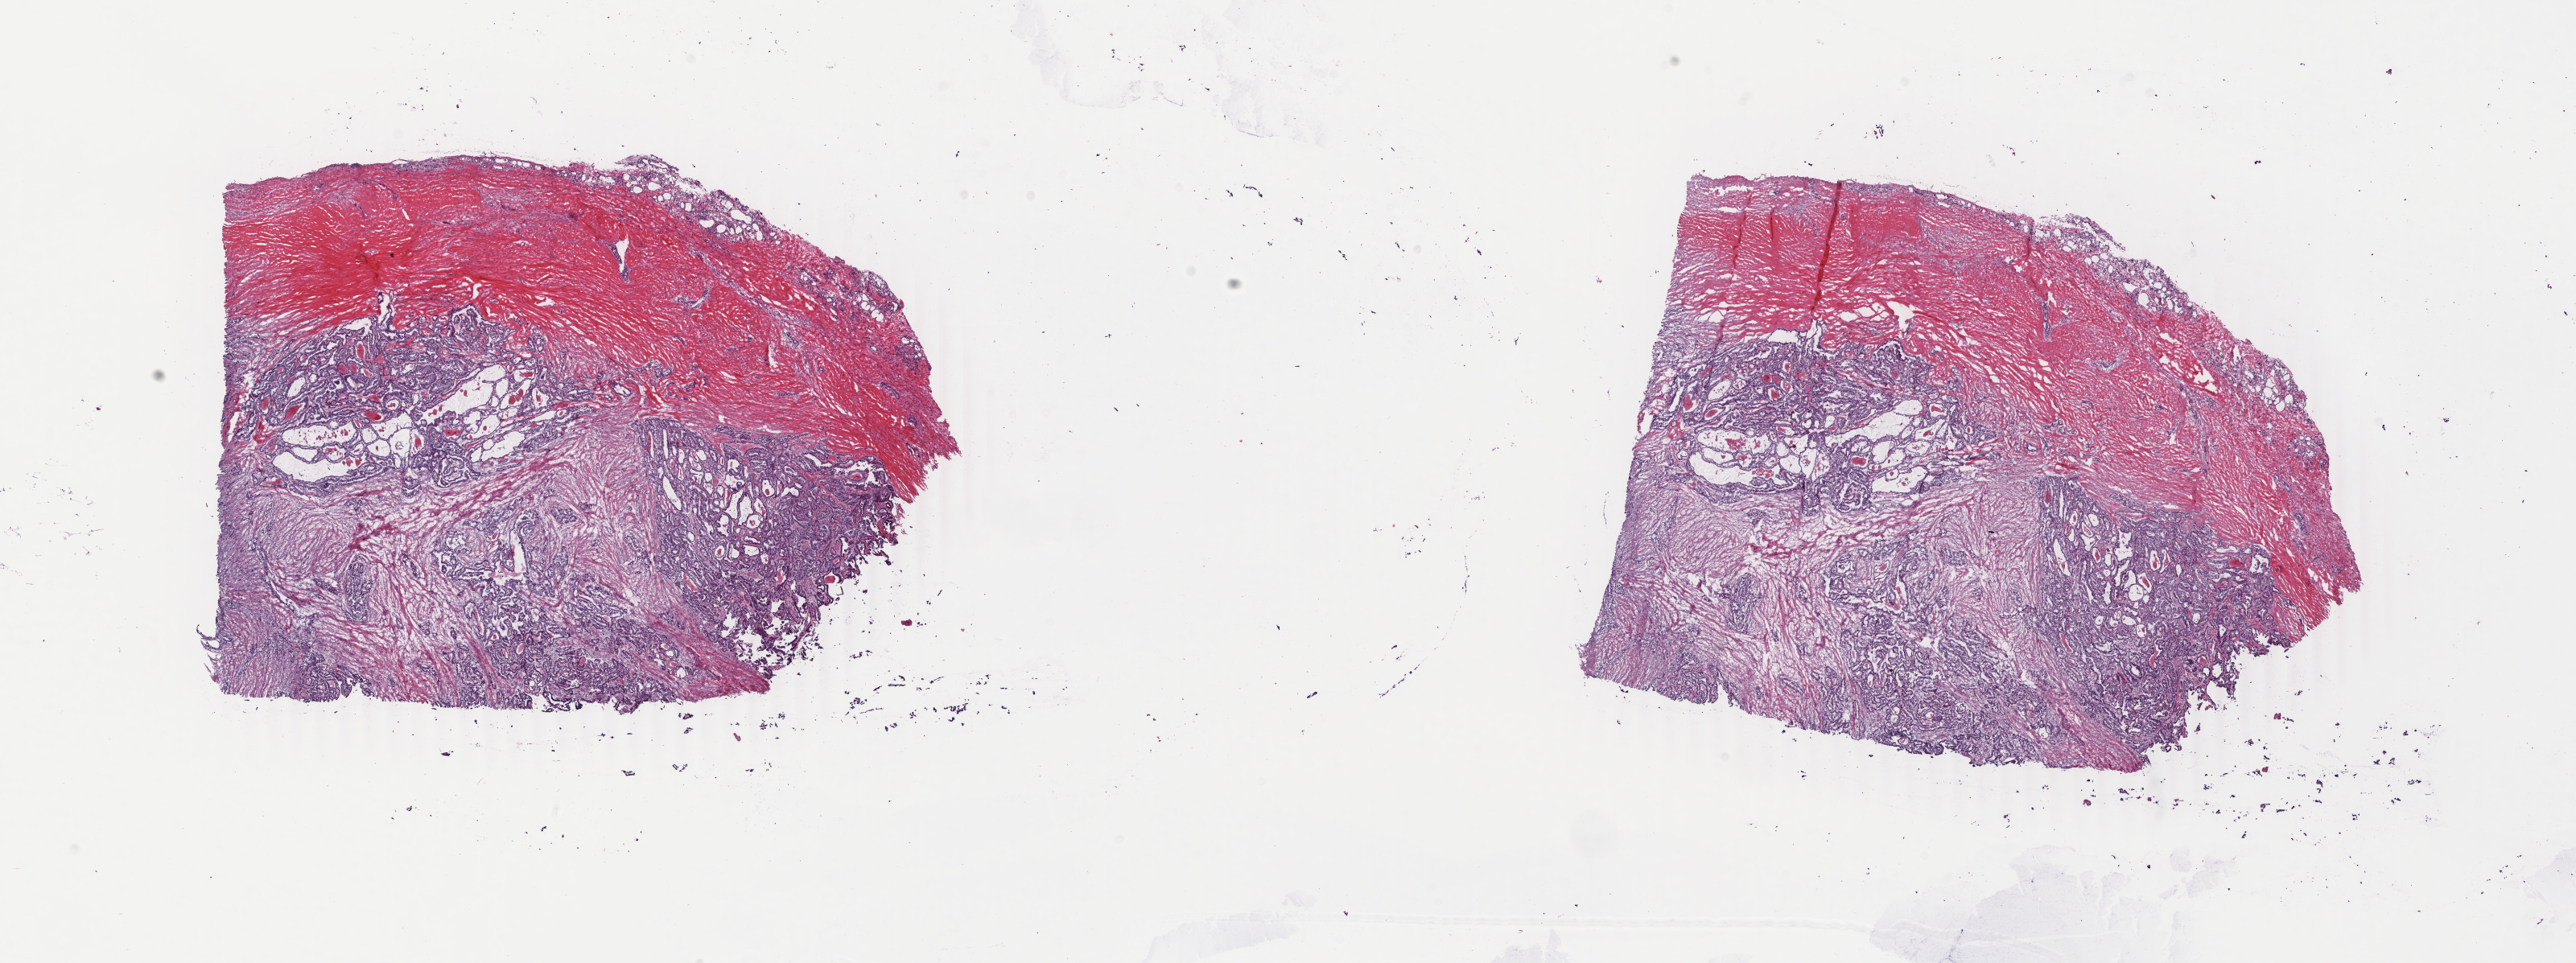
Whole-slide histology image, H&E — a low-resolution overview of the entire scanned area, about 25.5 x 9.5 mm; frozen section; thyroid, primary tumour sample. Patient: male, age at initial diagnosis 58 years. Pathologist review of this section (percent, as recorded): tumour cells 70%, tumour nuclei 70%, normal cells 0%, stromal cells 30%, necrosis 0%. Inflammatory infiltration, as recorded: lymphocyte infiltration 2%, monocyte infiltration 0%, neutrophil infiltration 1%.
TNM: T3 N1b MX. Histologic diagnosis: Papillary adenocarcinoma, NOS (thyroid gland). Laterality: bilateral. AJCC pathologic stage: IVA.